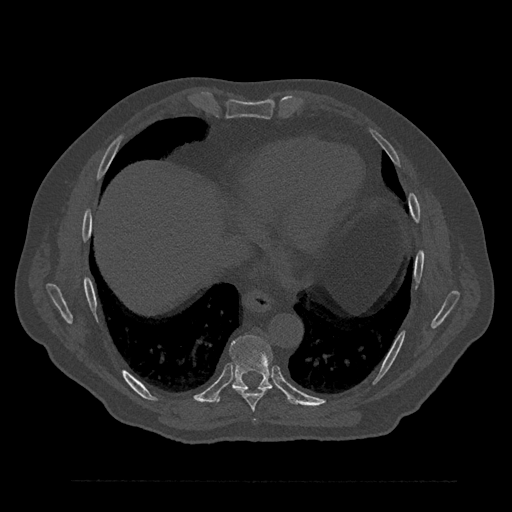
CT including the spine, one axial slice. Slice 431 of 797 in the series (ordered by position). Bone window (W 1800 / L 400 HU). 0.5 mm slice thickness. 512 × 512 image matrix, field of view 430 × 430 mm. Male patient, age 61 years. Case-level facts recorded for this patient, not image findings: primary cancer: prostate.
Structures marked on this image (semi-automatically segmented with operator editing):
- T8 vertebra: box from (x=231, y=386) to (x=269, y=412) px
- T9 vertebra: (x=215, y=335)–(x=288, y=404)